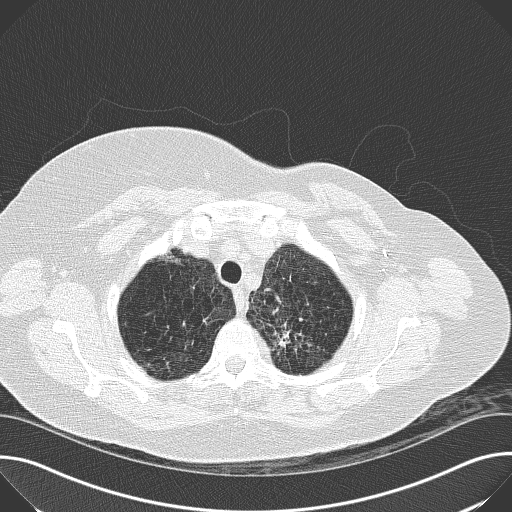
Low-dose screening chest CT, one axial slice. Slice 145 of 169 in the series (ordered by position). 120 kVp. Lung window (W 1500 / L -600 HU). 2 mm slice thickness. 512 × 512 image matrix, field of view 380 × 380 mm.
Outlined on this slice (outlined manually by an expert reader):
- lesion 1 (tumor, upper lobe of left lung): box from (x=274, y=331) to (x=289, y=348) px